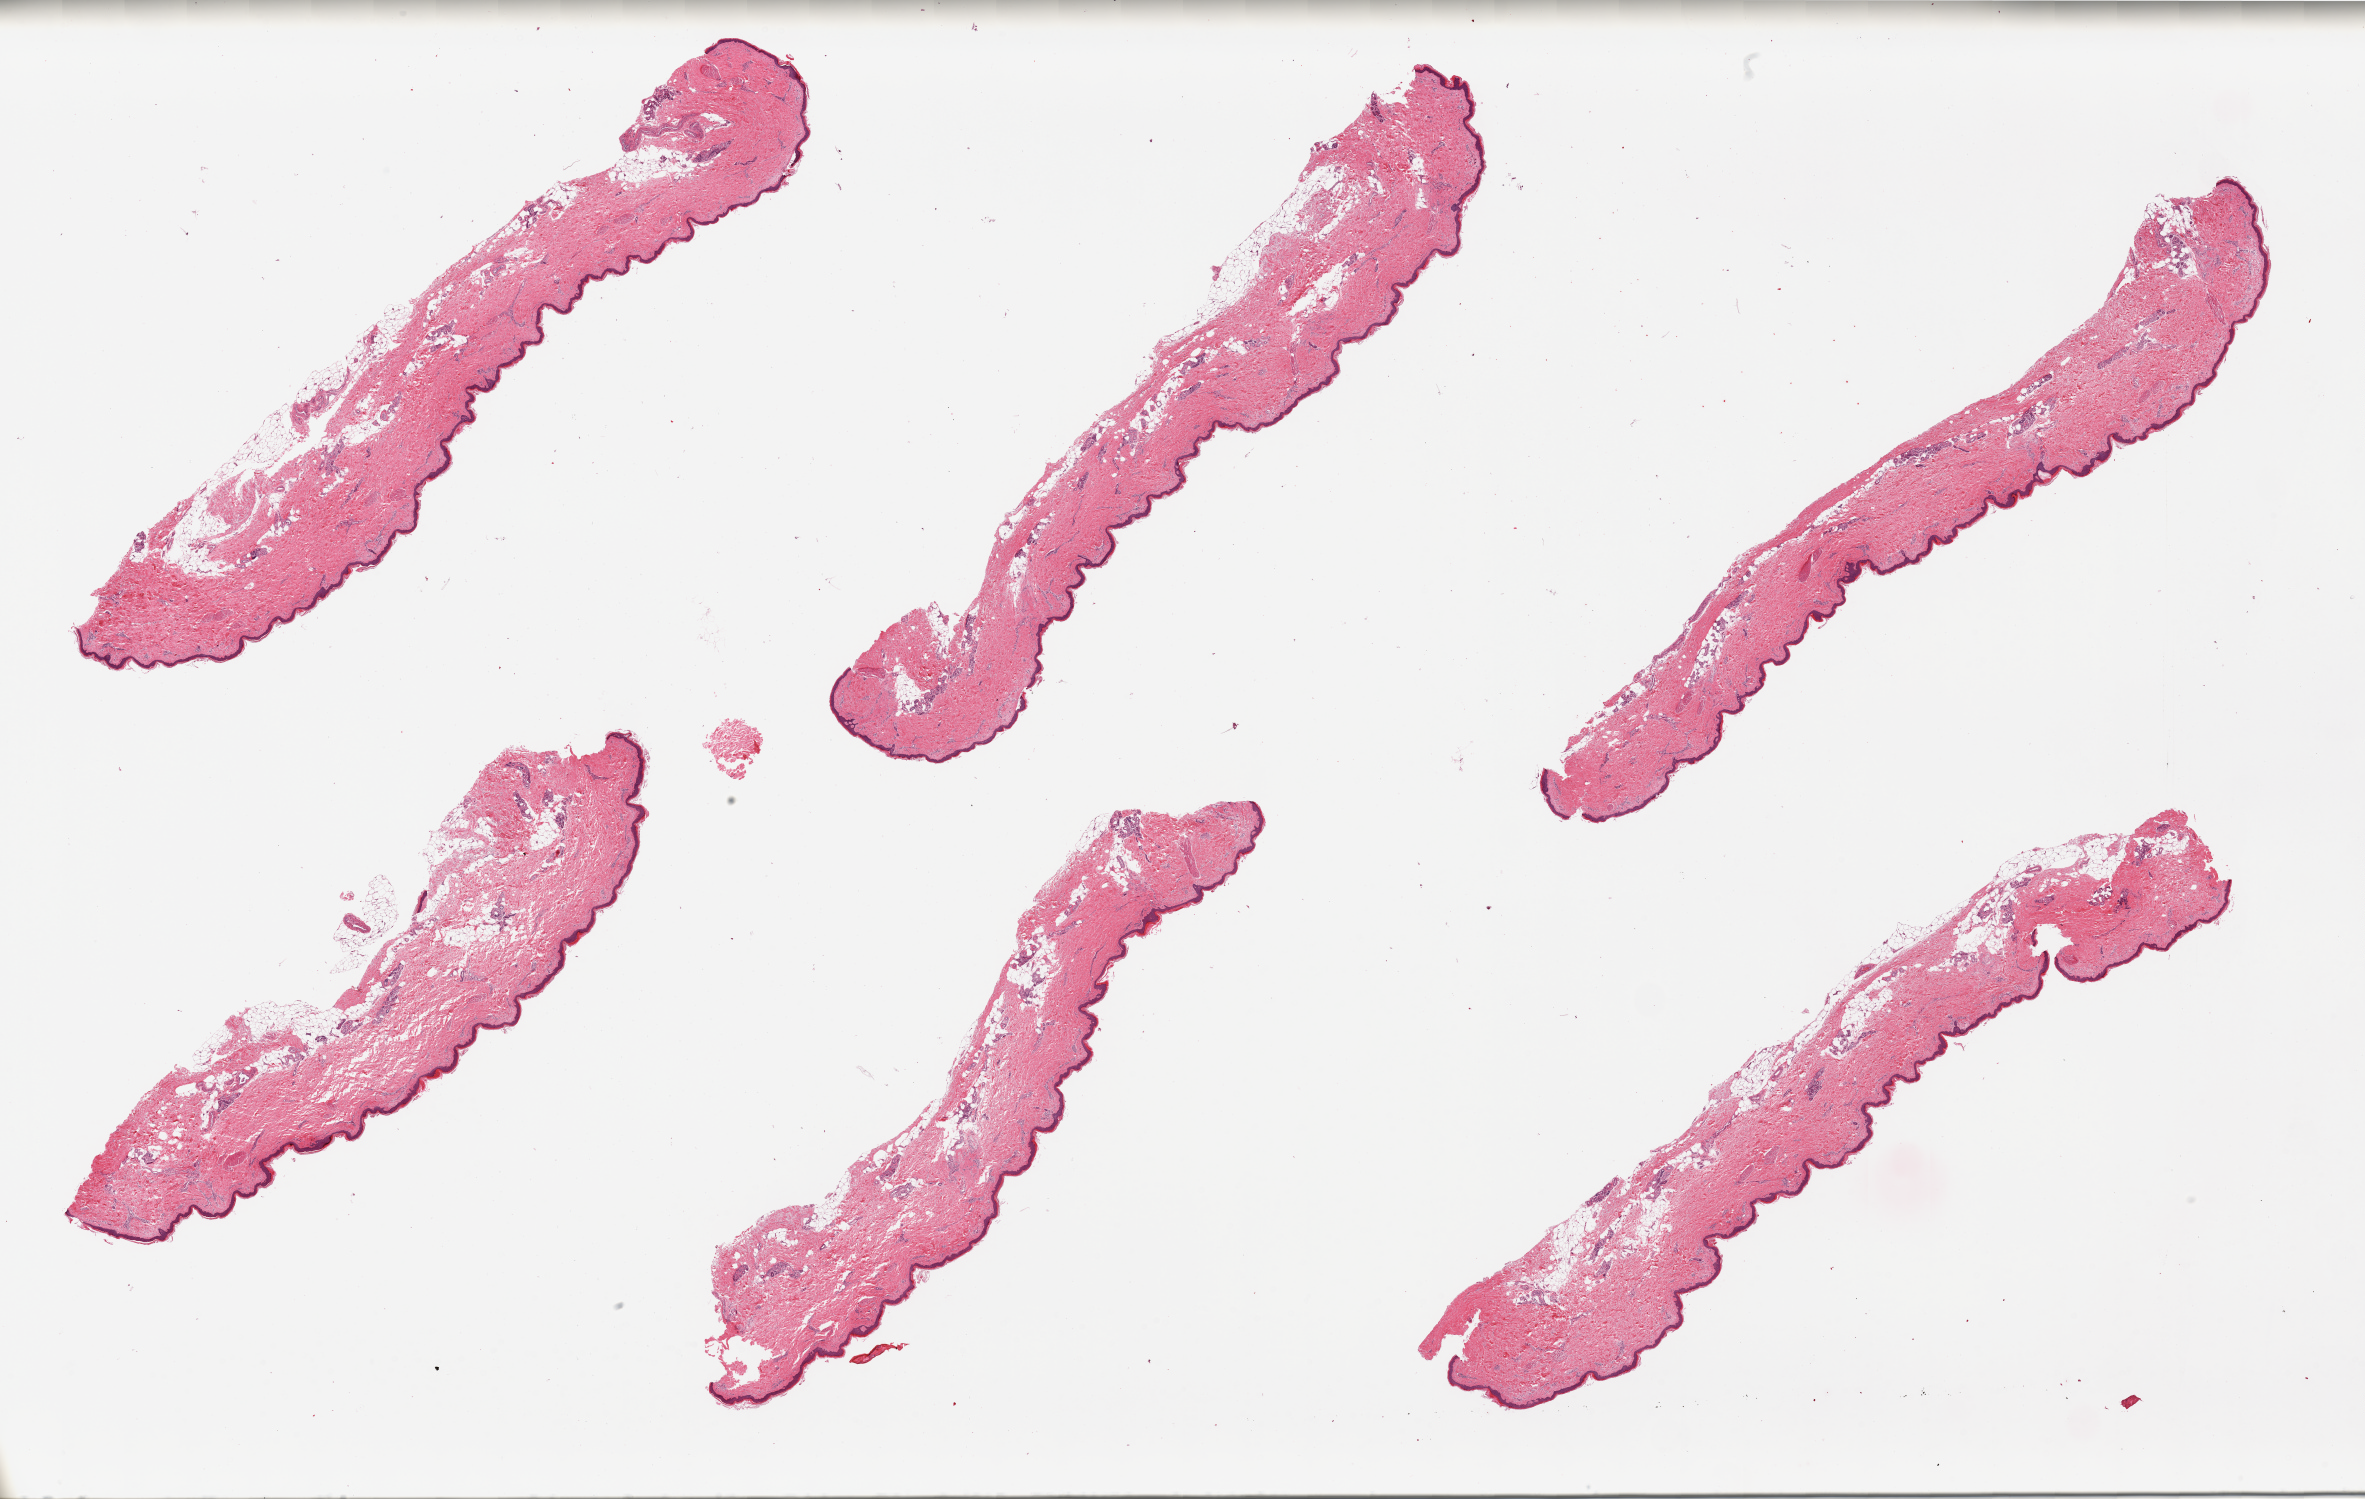
Hematoxylin and eosin (H&E) whole-slide image — low-resolution overview of the scanned area, about 37.4 x 23.7 mm, PAXgene-fixed, paraffin-embedded tissue, section of skin of lower leg (target tissue), donor tissue sample. Donor sex: male.
Review note (as recorded): 6 pieces. well trimmed.